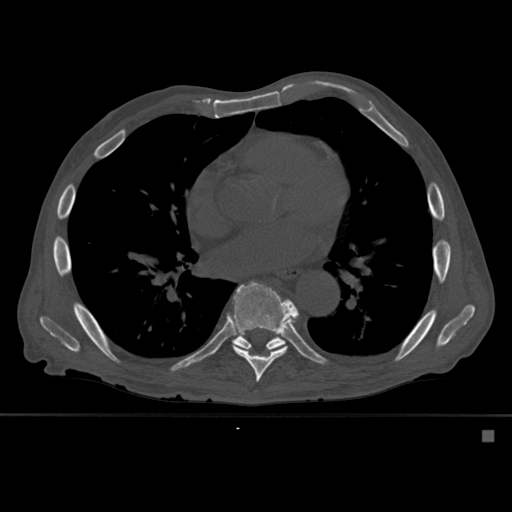
CT including the spine, one axial slice. Slice 345 of 527 in the series (ordered by position). Bone window (W 1800 / L 400 HU). 1.5 mm slice thickness. 512 × 512 image matrix, field of view 373 × 373 mm. Patient: male, 78 years. Case-level facts recorded for this patient, not image findings: primary cancer: prostate.
Annotated regions visible in this slice (semi-automatic segmentation, software-assisted and operator-edited):
- T8 vertebra: box from (x=227, y=281) to (x=299, y=383) px
- T9 vertebra: (x=232, y=332)–(x=286, y=352)